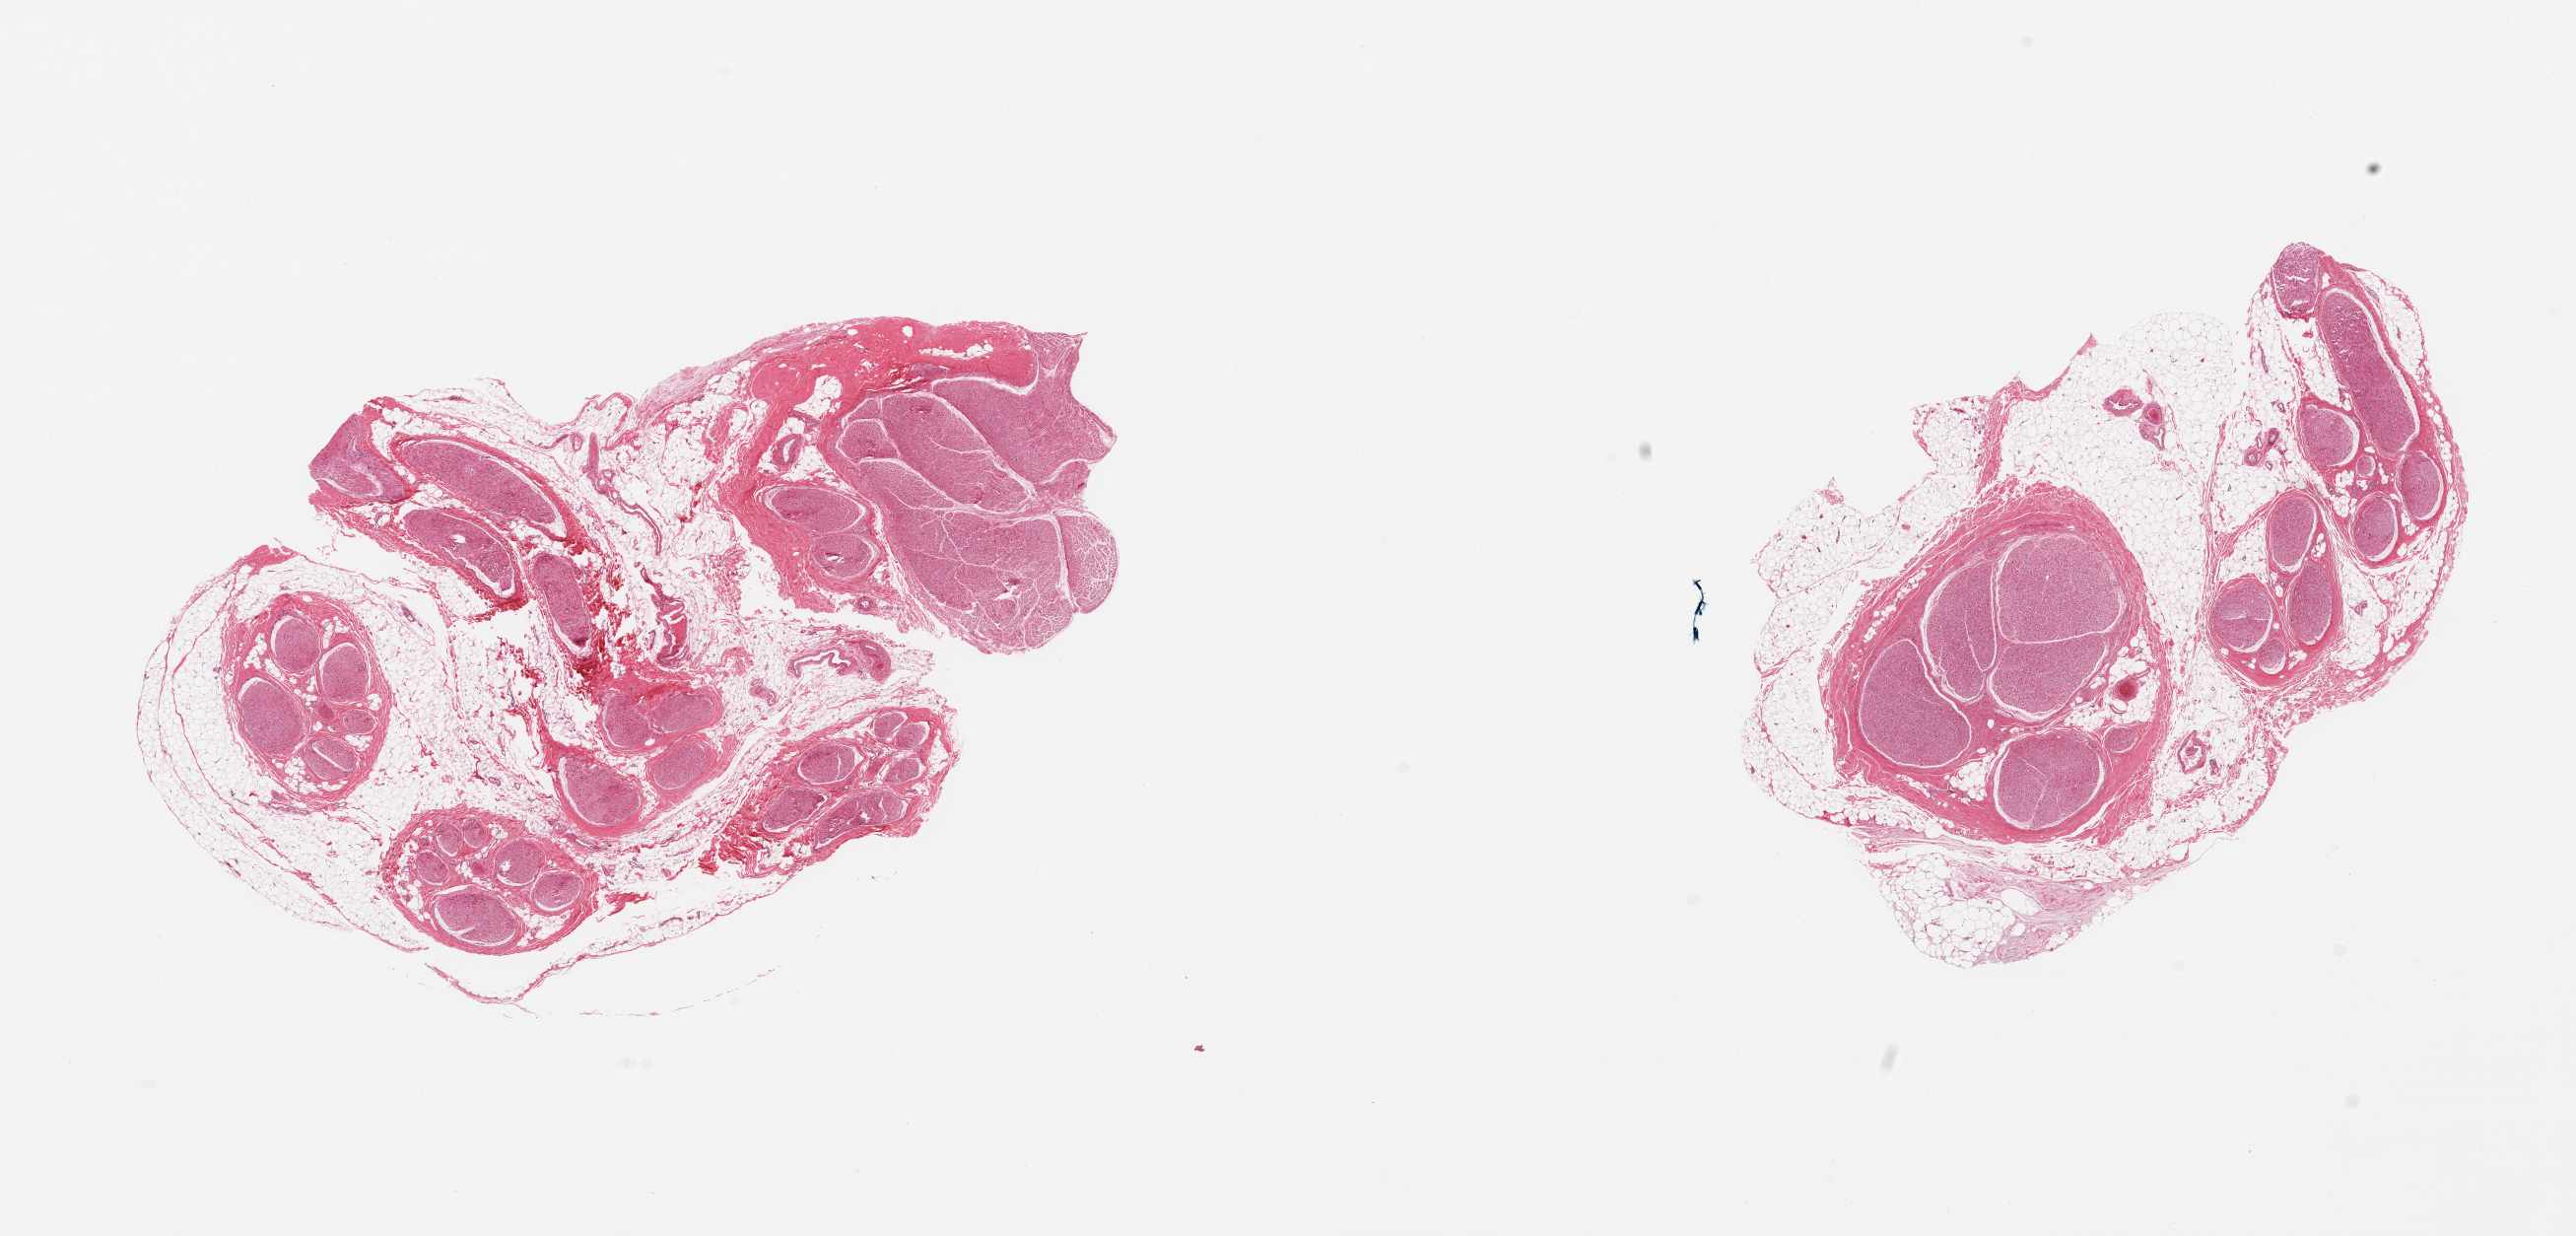
Whole-slide image, haematoxylin and eosin stain, whole scanned area (about 20.7 x 9.9 mm, from a 20x scan) shown as a low-resolution overview. PAXgene-fixed paraffin-embedded (PFPE) section. Sampled site (target tissue): tibial nerve. Donor tissue sample. Male donor.
Pathologist's review note for this sample: 2 pieces; nerve with 50-60% internal and attached fat.